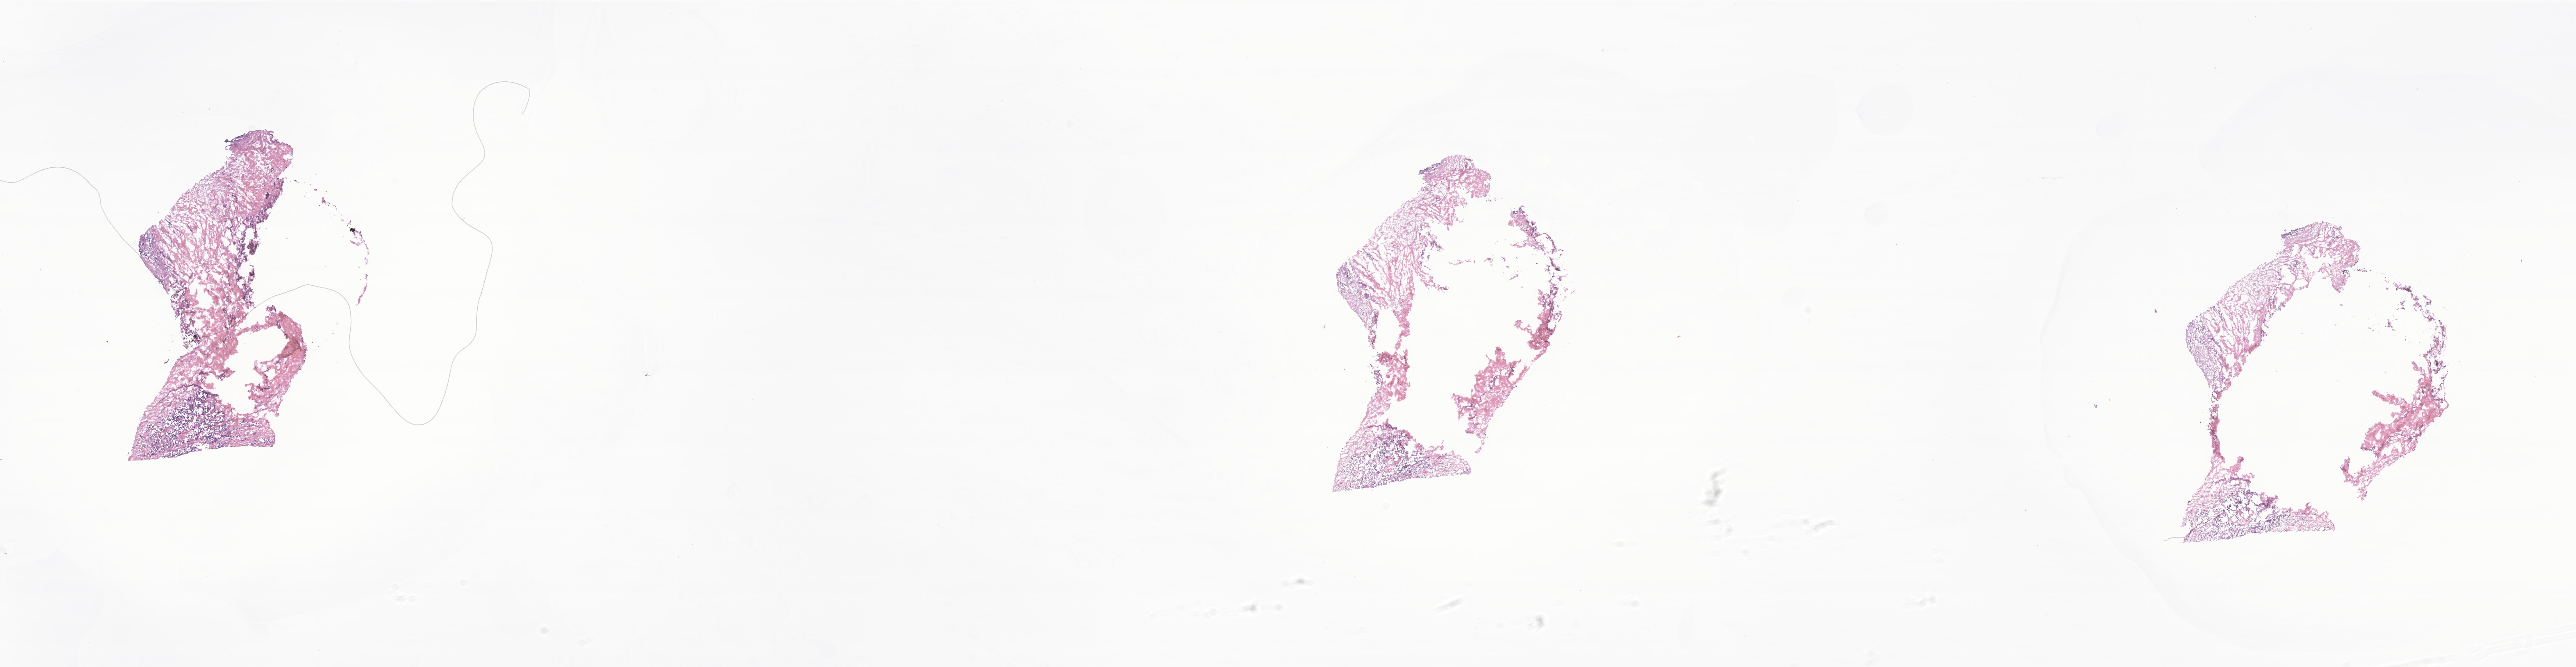
H&E whole-slide image of tumor tissue from the anus, shown as a low-resolution overview of the whole scanned area (about 37.4 x 9.7 mm); frozen section. Patient female; age 147 months.
• diagnosis (ICD-O-3 morphology term): Alveolar rhabdomyosarcoma